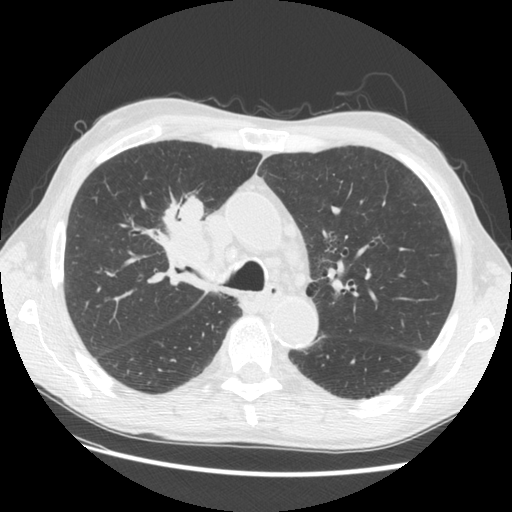
Chest CT (low-dose screening protocol), one axial image. Third screening round (two years after baseline). Lung window (W 1500 / L -600 HU). 2.5 mm slice thickness. Standard (soft-tissue) reconstruction kernel (STANDARD). 120 kVp. Slice 44 of 133 in the series. 512 × 512 image matrix, field of view 360 × 360 mm. Male, age 73 years at enrolment. Current smoker at enrolment.
Expert-annotated lung lesion, box from (x=141, y=185) to (x=234, y=275) px. The screening reader recorded 4 non-calcified nodules or masses ≥4 mm on this exam (right upper lobe, right upper lobe, right upper lobe, left lower lobe); which of them this box marks is not recorded. Official screen result: positive, other. Later outcome: lung cancer diagnosed 48 days after this screen — squamous cell carcinoma, NOS, right upper lobe, poorly differentiated (G3), stage IIIB (AJCC 6th edition), 56 mm at pathology.